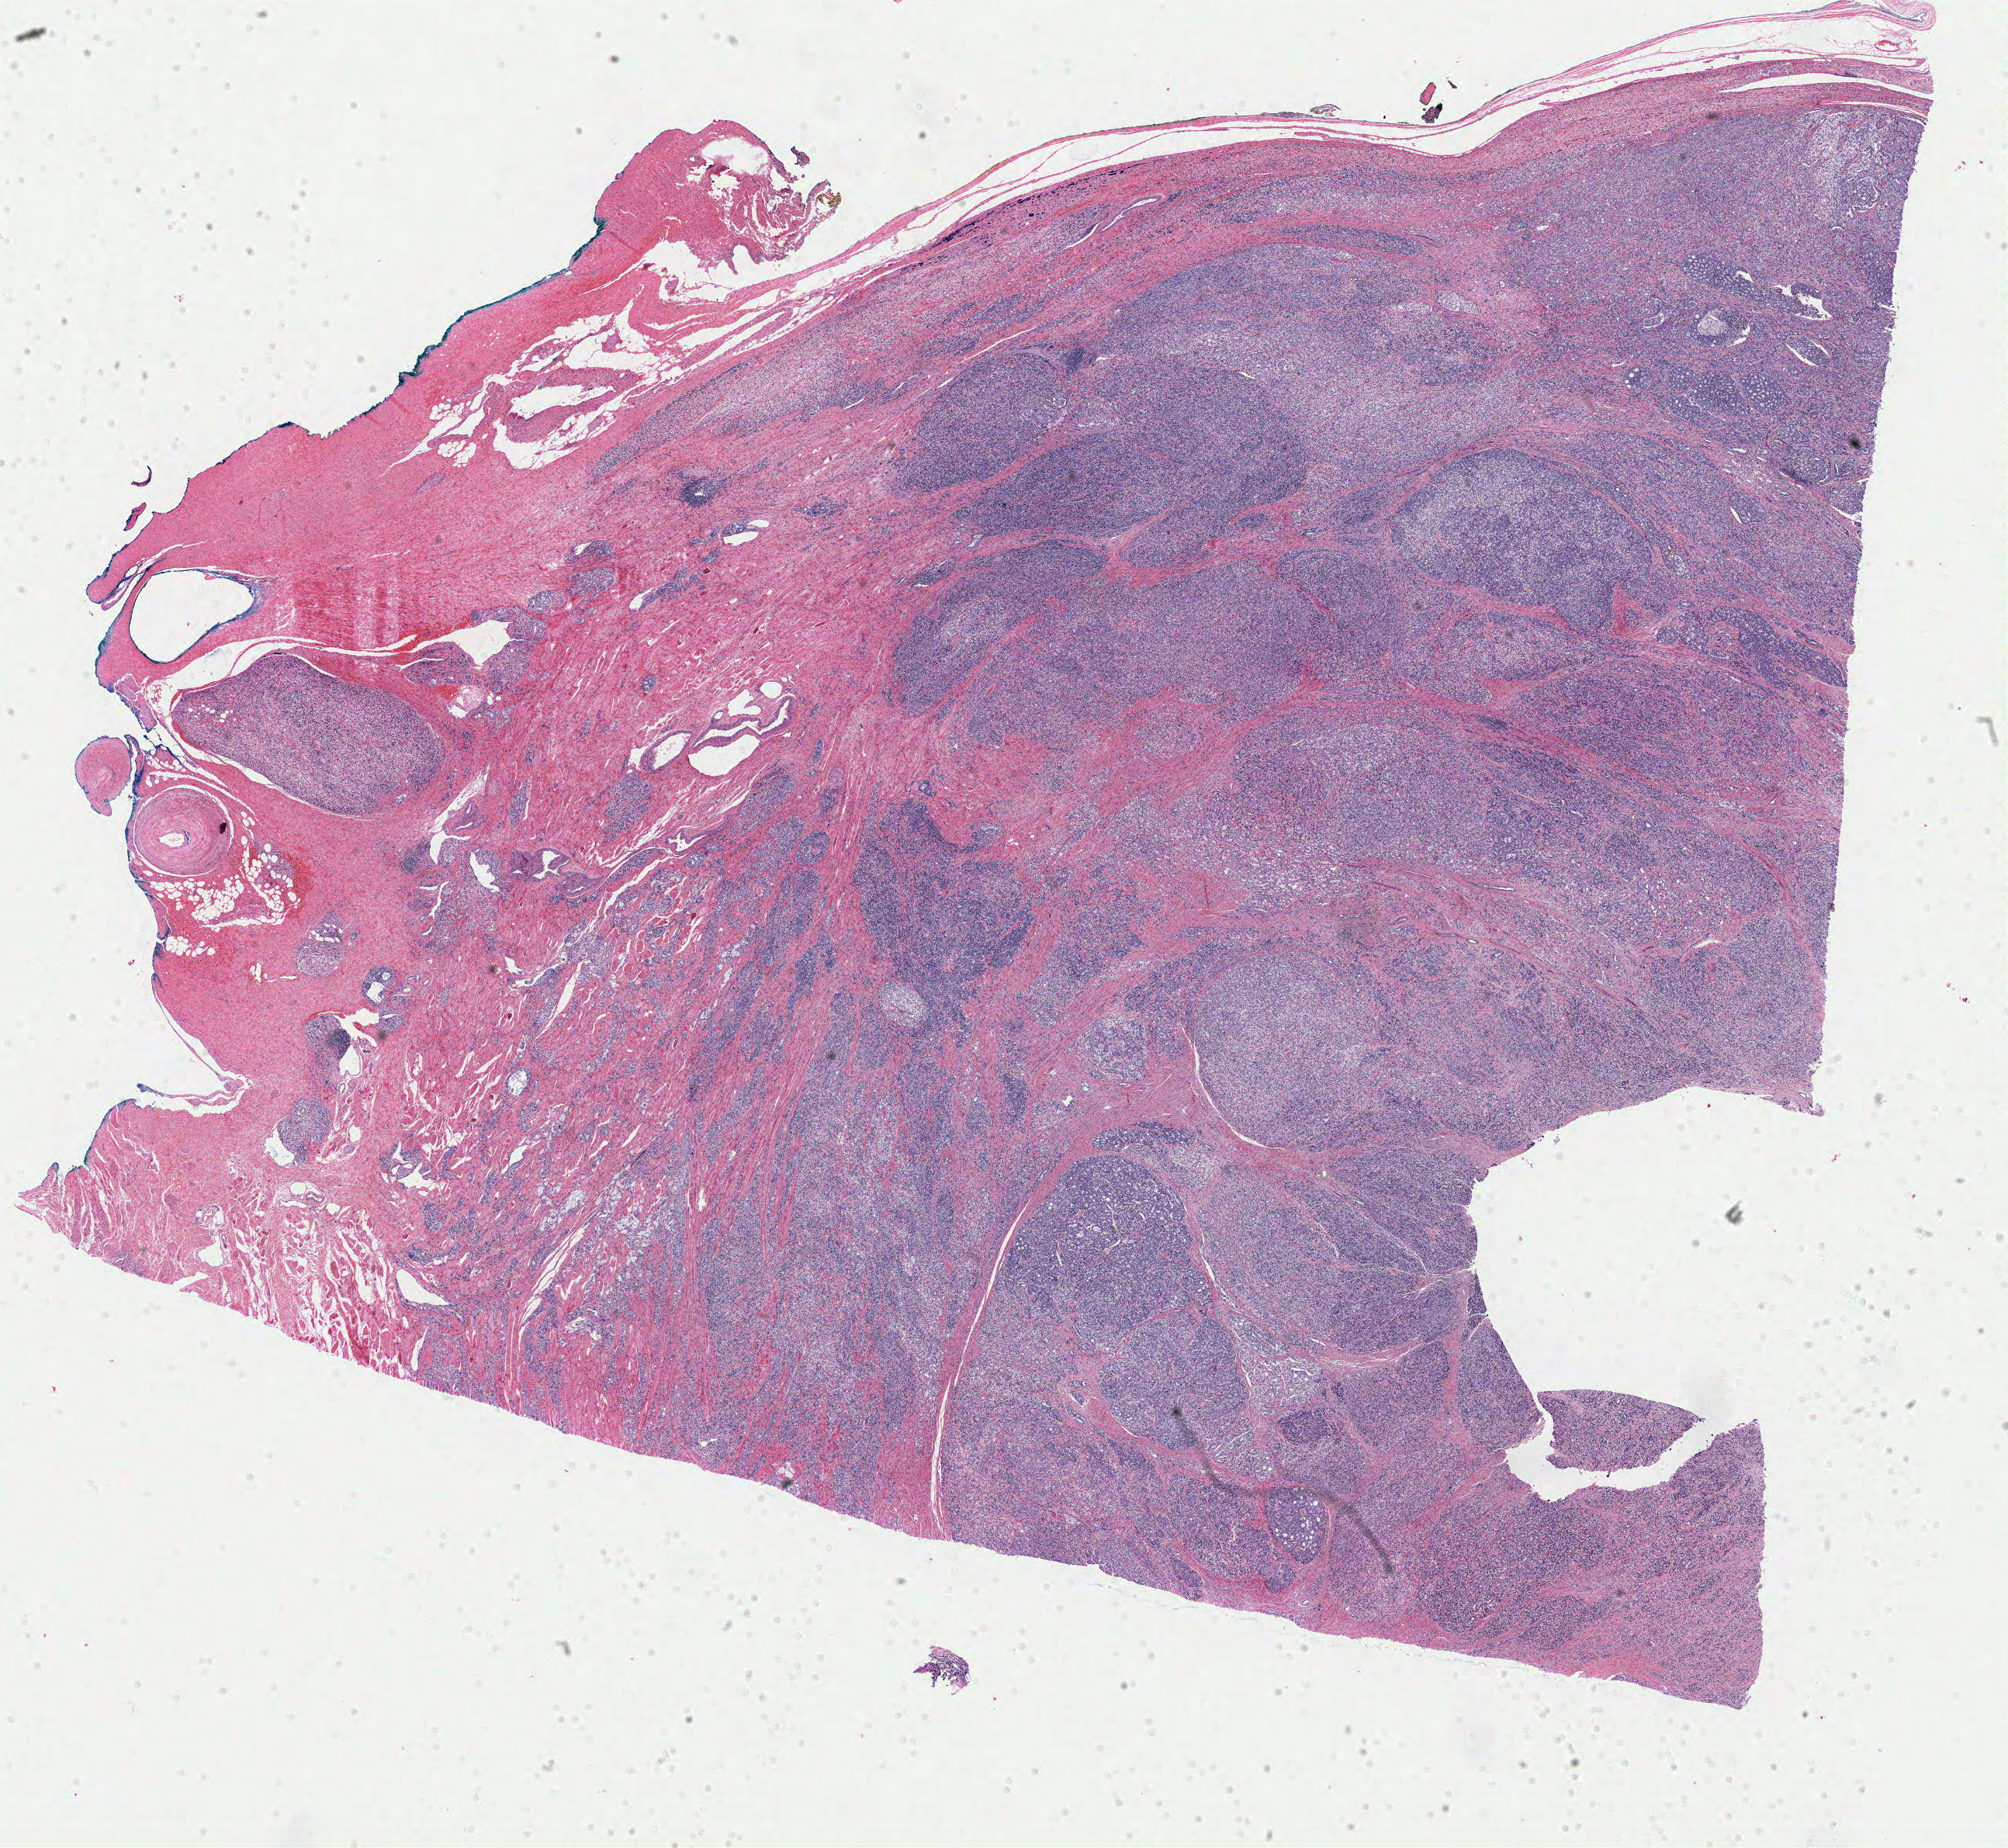
Digitized H&E-stained tissue section (whole slide), low-resolution overview of the scanned area, about 20.4 x 18.8 mm (from a 40x scan). Formalin-fixed paraffin-embedded (FFPE) diagnostic section. Prostate, primary tumour sample. Patient: male, age at initial diagnosis 72 years.
Pathologic diagnosis: Adenocarcinoma, NOS.